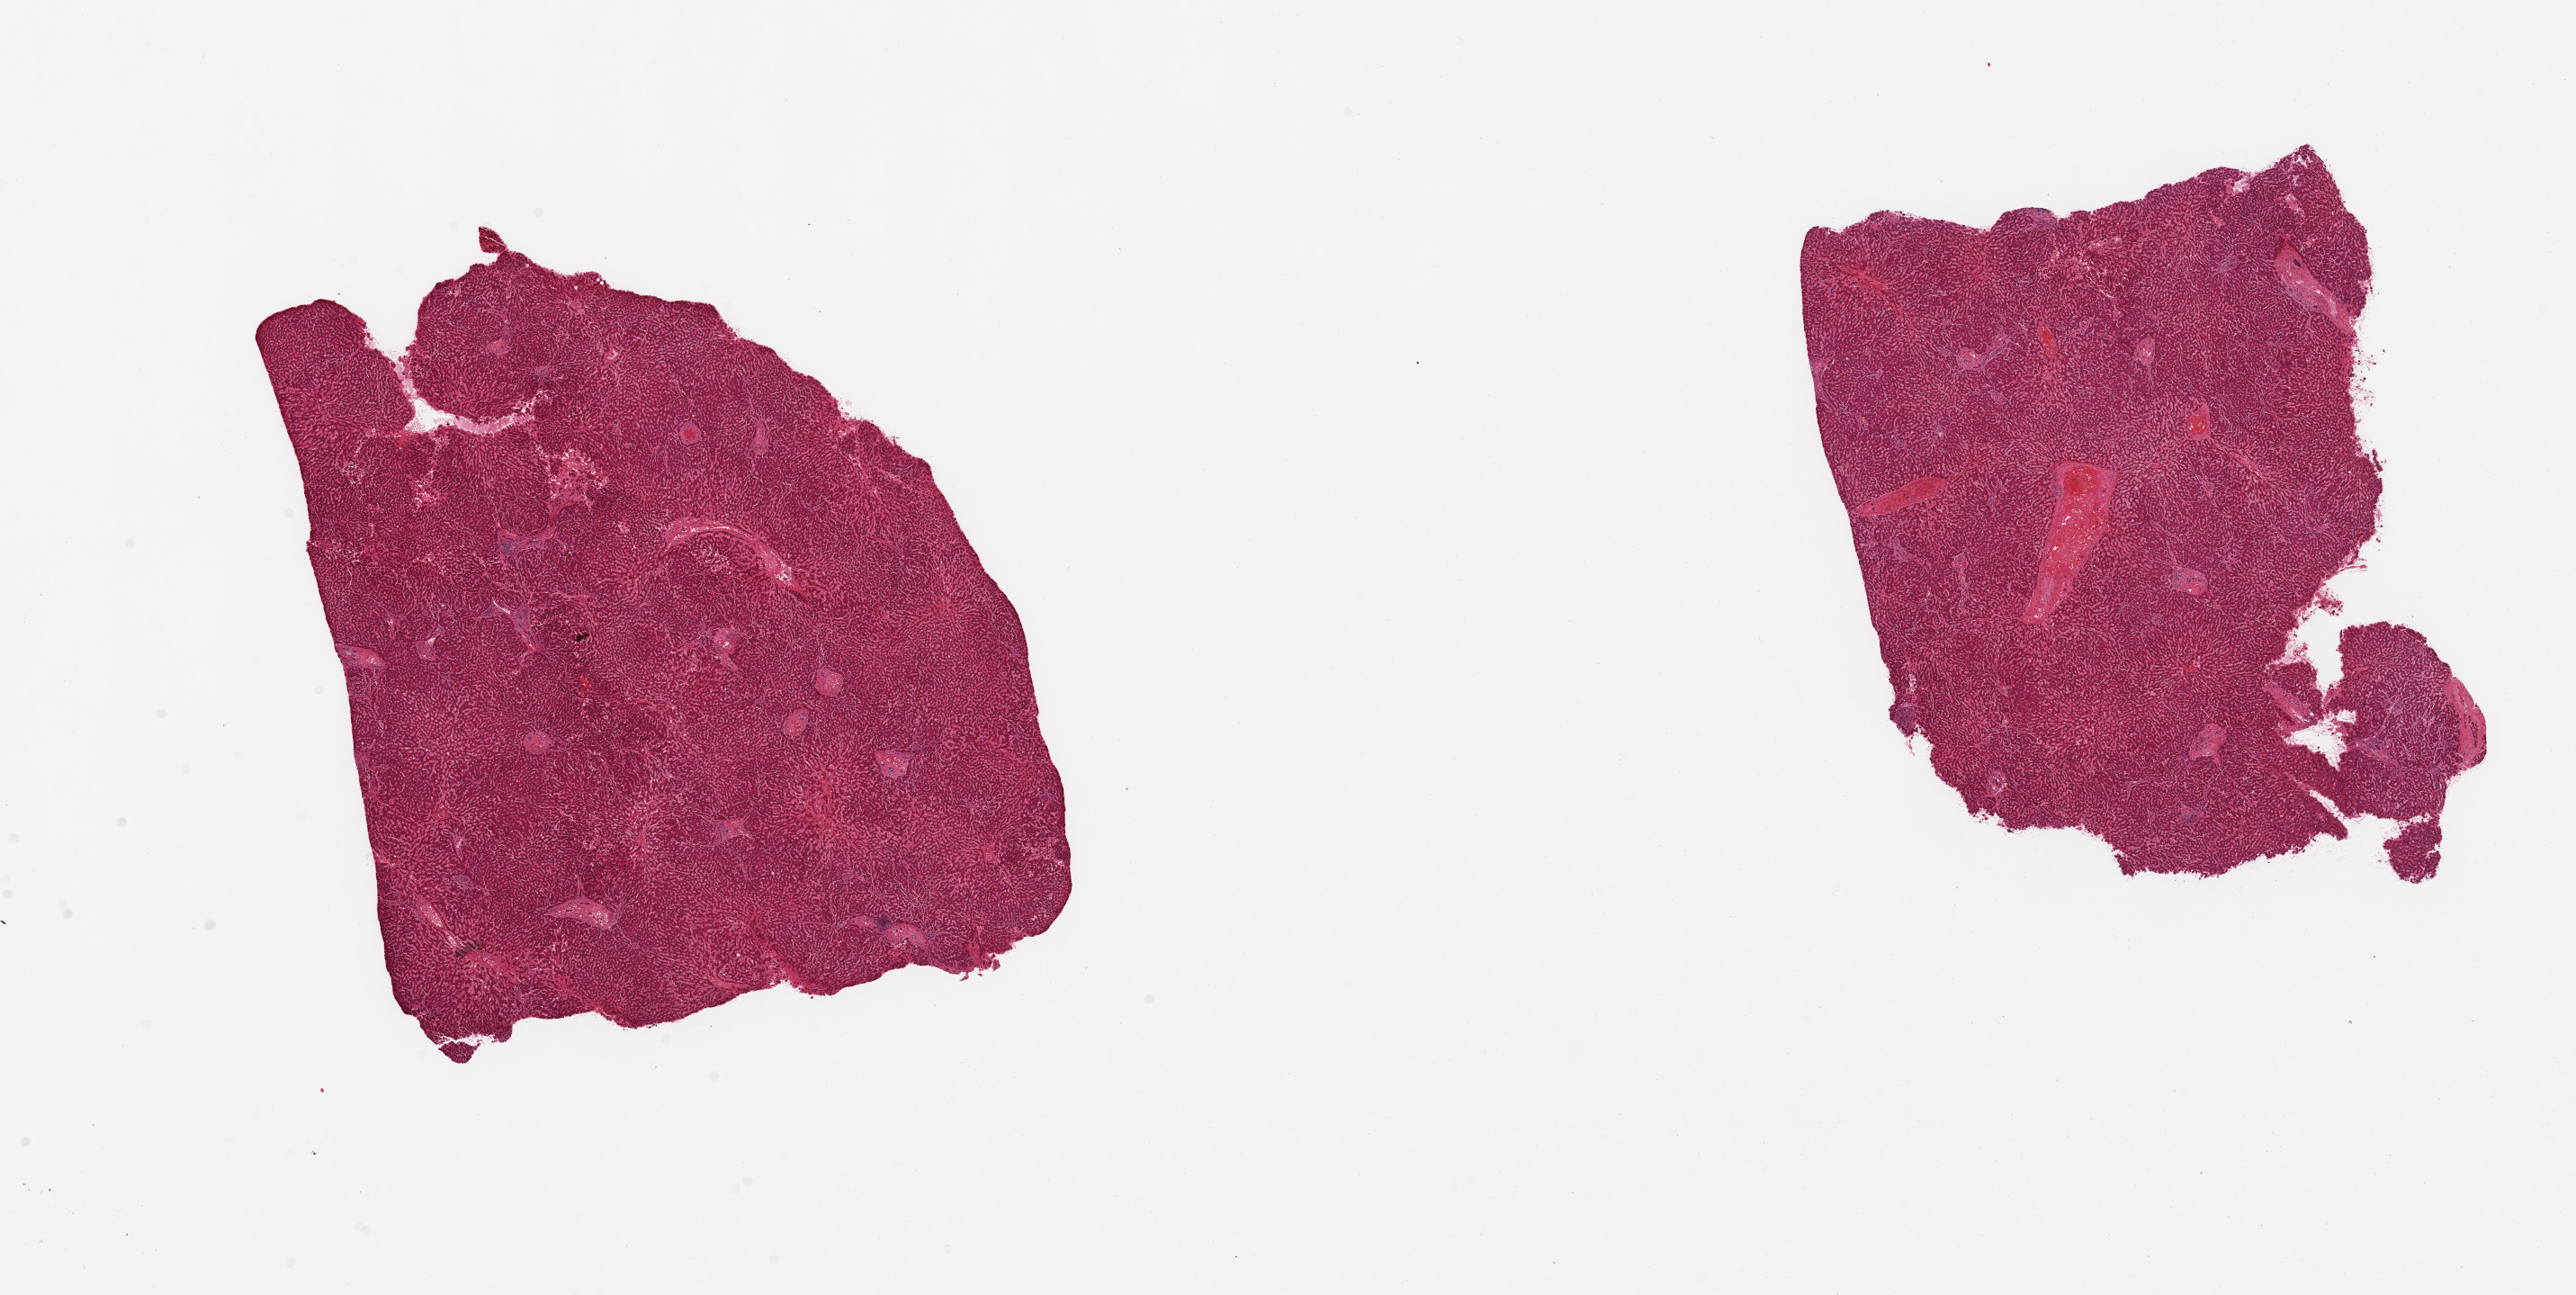
Haematoxylin and eosin whole-slide image — low-resolution overview of the scanned area, about 22.6 x 11.4 mm. PAXgene-fixed, paraffin-embedded tissue. Sampled site (target tissue): liver. Tissue donor sample. Donor: male.
* reviewer comment on this tissue sample: 2 pieces; mild central congestion and atrophy